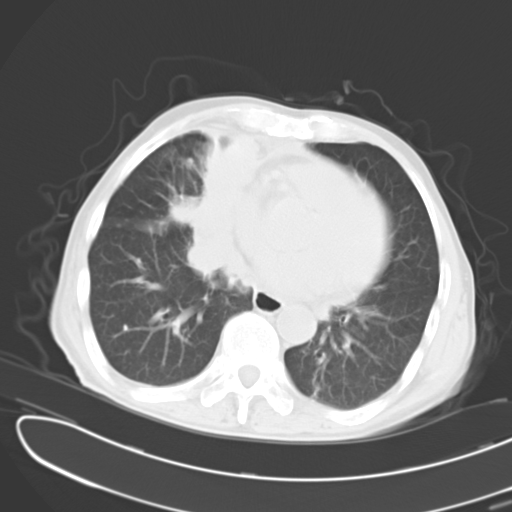
Chest CT, one axial slice; slice 7 of 24 in the series (ordered by position); reconstruction kernel B40f; 120 kVp; lung window (W 1500 / L -600 HU); 10 mm slice thickness; 512 × 512 image matrix, field of view 353 × 353 mm. Male patient, age 65 years. From the clinical record (not read from this slice): clinical TNM (as recorded): T2 N3 M1.
Outlined on this slice (rectangle marked by the reading radiologist):
- lung tumour (recorded histology: small cell carcinoma): bounding box <172,112,264,279> (left, top, right, bottom; pixels)